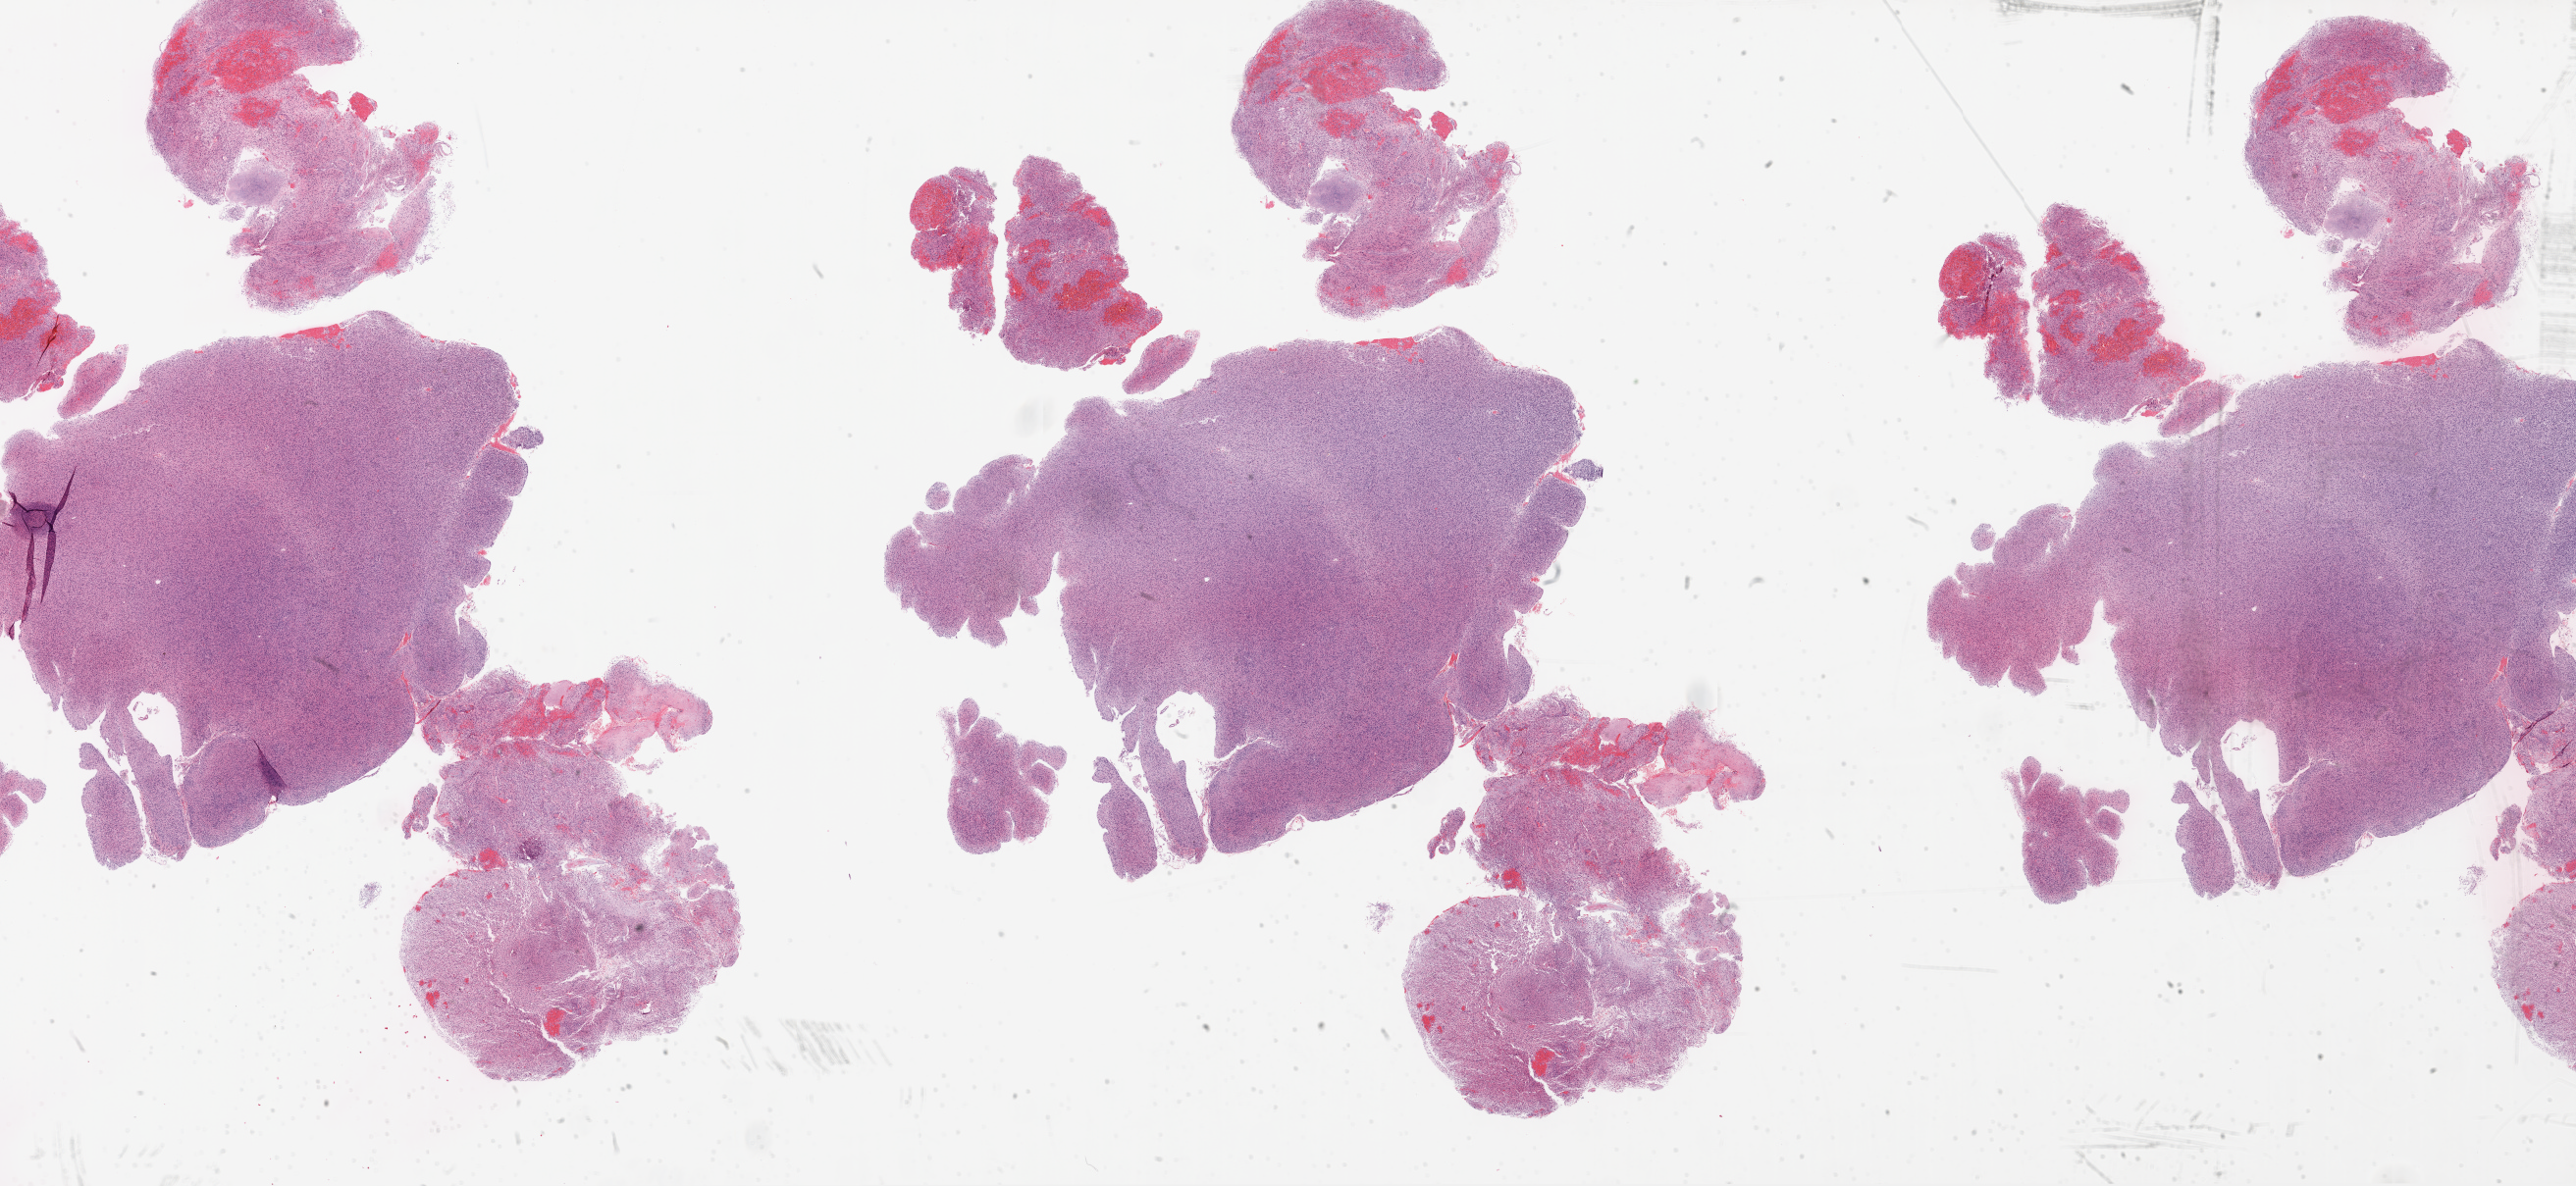
Whole-slide histology image, H&E-stained — whole scanned area (about 42.1 x 19.4 mm, slide scanned at 20x) shown as a low-resolution overview, formalin-fixed paraffin-embedded (FFPE) diagnostic section, brain, primary tumour sample. Female patient; age at initial diagnosis 58 years.
* diagnosis: Glioblastoma